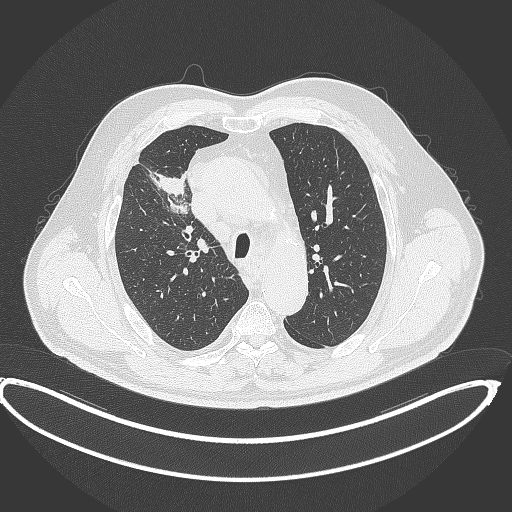
Chest CT, one axial slice. Position 295 of 390 along the scan axis. Reconstruction kernel B70f. 120 kVp. Lung window (W 1500 / L -600 HU). 1 mm slice thickness. 512 × 512 image matrix, field of view 448 × 448 mm. Male patient, age 62 years. Case-level facts recorded for this patient, not image findings: clinical TNM (as recorded): T1c N3 M1c.
Annotated regions visible in this slice (rectangle marked by the reading radiologist):
- lung tumour (recorded histology: adenocarcinoma): bounding box <151,169,188,216> (left, top, right, bottom; pixels)